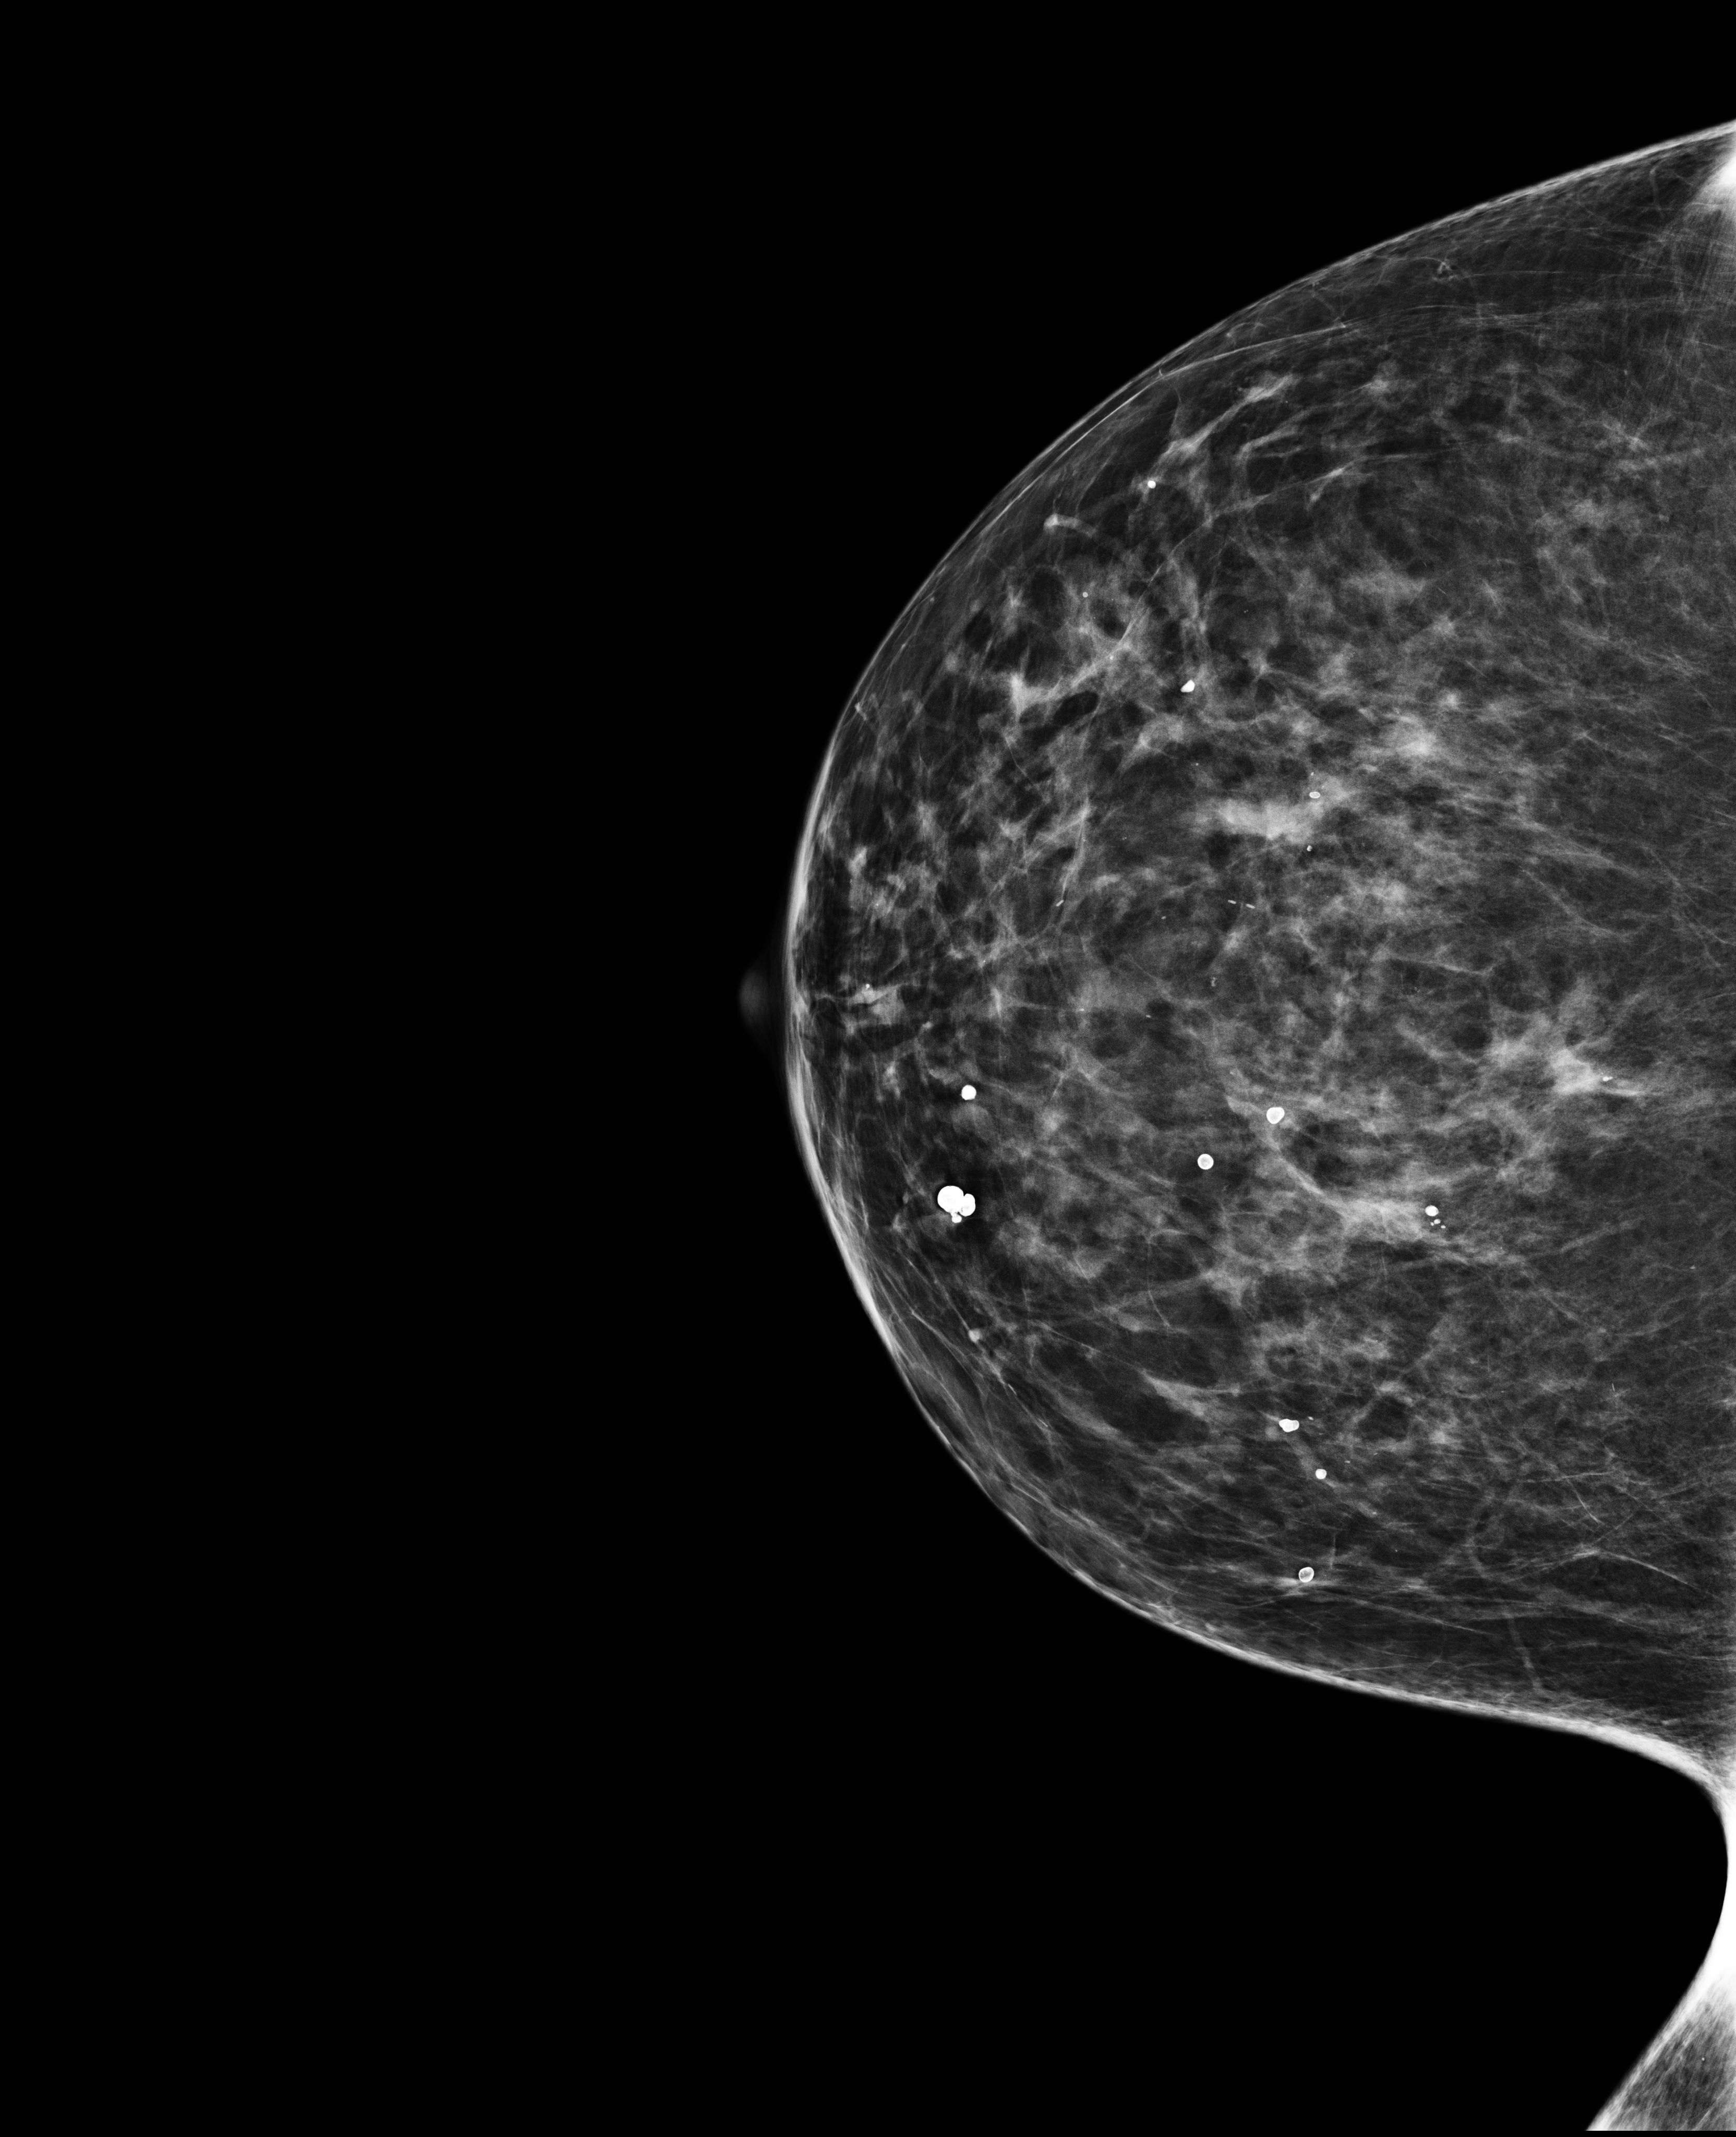
Screening examination, compressed breast thickness 66 mm, system: Selenia Dimensions. Patient aged 66 years (female).
Image type: full-field digital mammogram. Breast: right. Projection: CC view.